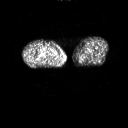
FDG PET of an extremity soft-tissue mass (from a PET/CT study), one axial slice. Slice 233 of 311 in the series (ordered by position). 128 × 128 image matrix, field of view 700 × 700 mm. Male patient, age 50 years. From the clinical record (not read from this slice): histological type: undifferentiated - pleiomorphic; grade: high; site of the primary tumour: right thigh.
Structures marked on this image (expert contour drawn on MRI and transferred to this co-registered scan by the dataset authors):
- gross tumour volume including surrounding oedema: bounding box [x1, y1, x2, y2] px = [42, 52, 47, 57]